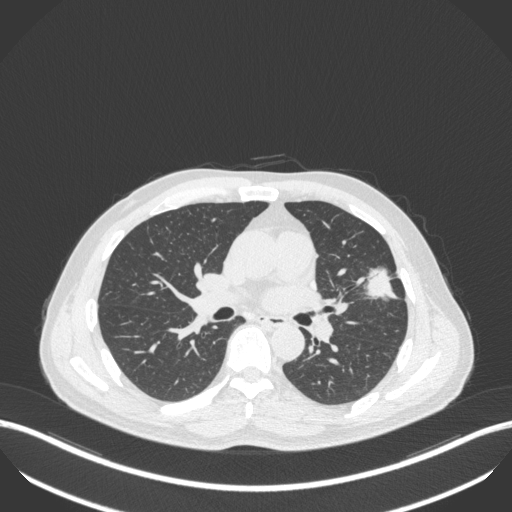
Chest CT, one axial slice; position 219 of 418 along the scan axis; reconstruction kernel B31f; lung window (W 1500 / L -600 HU); 1 mm slice thickness; 512 × 512 image matrix. Male patient, age 55 years. Case-level facts recorded for this patient, not image findings: clinical TNM (as recorded): T1c N0 M0.
Structures marked on this image (rectangle marked by the reading radiologist):
- lung tumour (recorded histology: adenocarcinoma): bounding box [x1, y1, x2, y2] px = [358, 264, 399, 305]